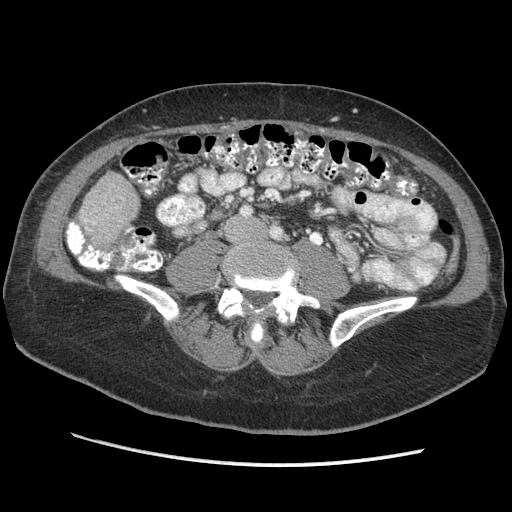
Contrast-enhanced abdominal CT (liver protocol), one axial slice. Slice 81 of 170 in the series (ordered by position). Reconstruction kernel STANDARD. 140 kVp. Soft-tissue window (W 400 / L 40 HU). 2.5 mm slice thickness. 512 × 512 image matrix. Case-level facts recorded for this patient, not image findings: diagnosis: hepatocellular carcinoma (patient treated with transarterial chemoembolisation; whether this scan precedes or follows treatment is not stated here); TNM stage (as recorded): Stage-II; Child-Pugh class: A.
Outlined on this slice (semi-automatically segmented with operator editing):
- liver parenchyma outside the tumour (the mass and vessels are separate outlines, so this box may not span the whole liver): box from (x=78, y=172) to (x=138, y=244) px